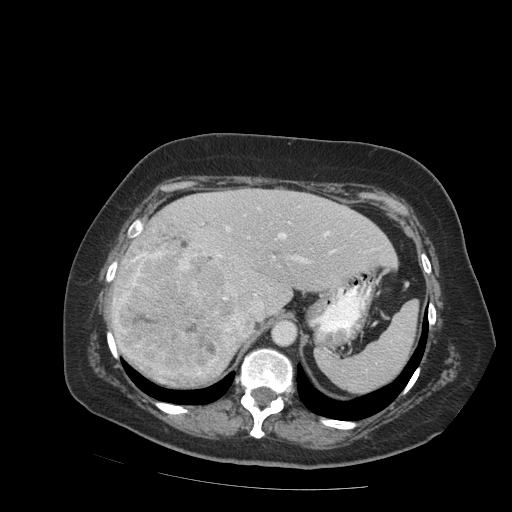
Contrast-enhanced abdominal CT (liver protocol), one axial slice. Slice 61 of 99 in the series (ordered by position). Reconstruction kernel STANDARD. 140 kVp. Soft-tissue window (W 400 / L 40 HU). 2.5 mm slice thickness. 512 × 512 image matrix. From the clinical record (not read from this slice): diagnosis: hepatocellular carcinoma (patient treated with transarterial chemoembolisation; whether this scan precedes or follows treatment is not stated here); TNM stage (as recorded): Stage-IVB; Child-Pugh class: A.
Outlined on this slice (semi-automatically segmented with operator editing):
- abdominal aorta: bounding box (x1, y1, x2, y2) in pixels: (273, 321, 295, 345)
- liver parenchyma outside the tumour (the mass and vessels are separate outlines, so this box may not span the whole liver): (110, 188, 398, 341)
- mass: (115, 225, 252, 387)
- liver vessels: (133, 208, 336, 306)